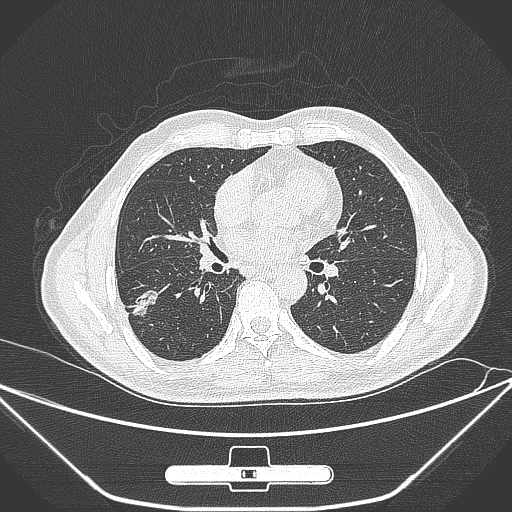
Chest CT, one axial slice. 120 kVp. Lung window (W 1500 / L -600 HU). 512 × 512 image matrix, field of view 398 × 398 mm. Male patient, age 71 years. From the clinical record (not read from this slice): clinical TNM (as recorded): T1c N0 M0; histopathological grade: G2.
Annotated regions visible in this slice (bounding box drawn by a radiologist):
- lung tumour (recorded histology: adenocarcinoma): bounding box (x1, y1, x2, y2) in pixels: (126, 286, 160, 328)